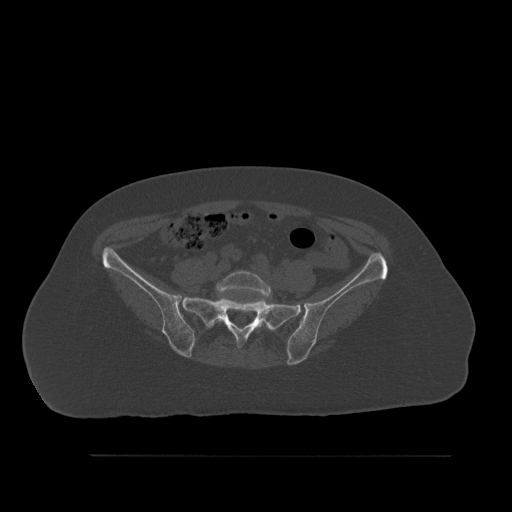
CT including the spine, one axial slice. Slice 178 of 527 in the series (ordered by position). Bone window (W 1800 / L 400 HU). 1.5 mm slice thickness. 512 × 512 image matrix, field of view 470 × 470 mm. Patient: female, 73 years. Case-level facts recorded for this patient, not image findings: primary cancer: breast; vertebrae with lytic lesions (as recorded): L2.
Structures marked on this image (semi-automatically segmented with operator editing):
- L5 vertebra: bounding box (x1, y1, x2, y2) in pixels: (216, 270, 273, 331)